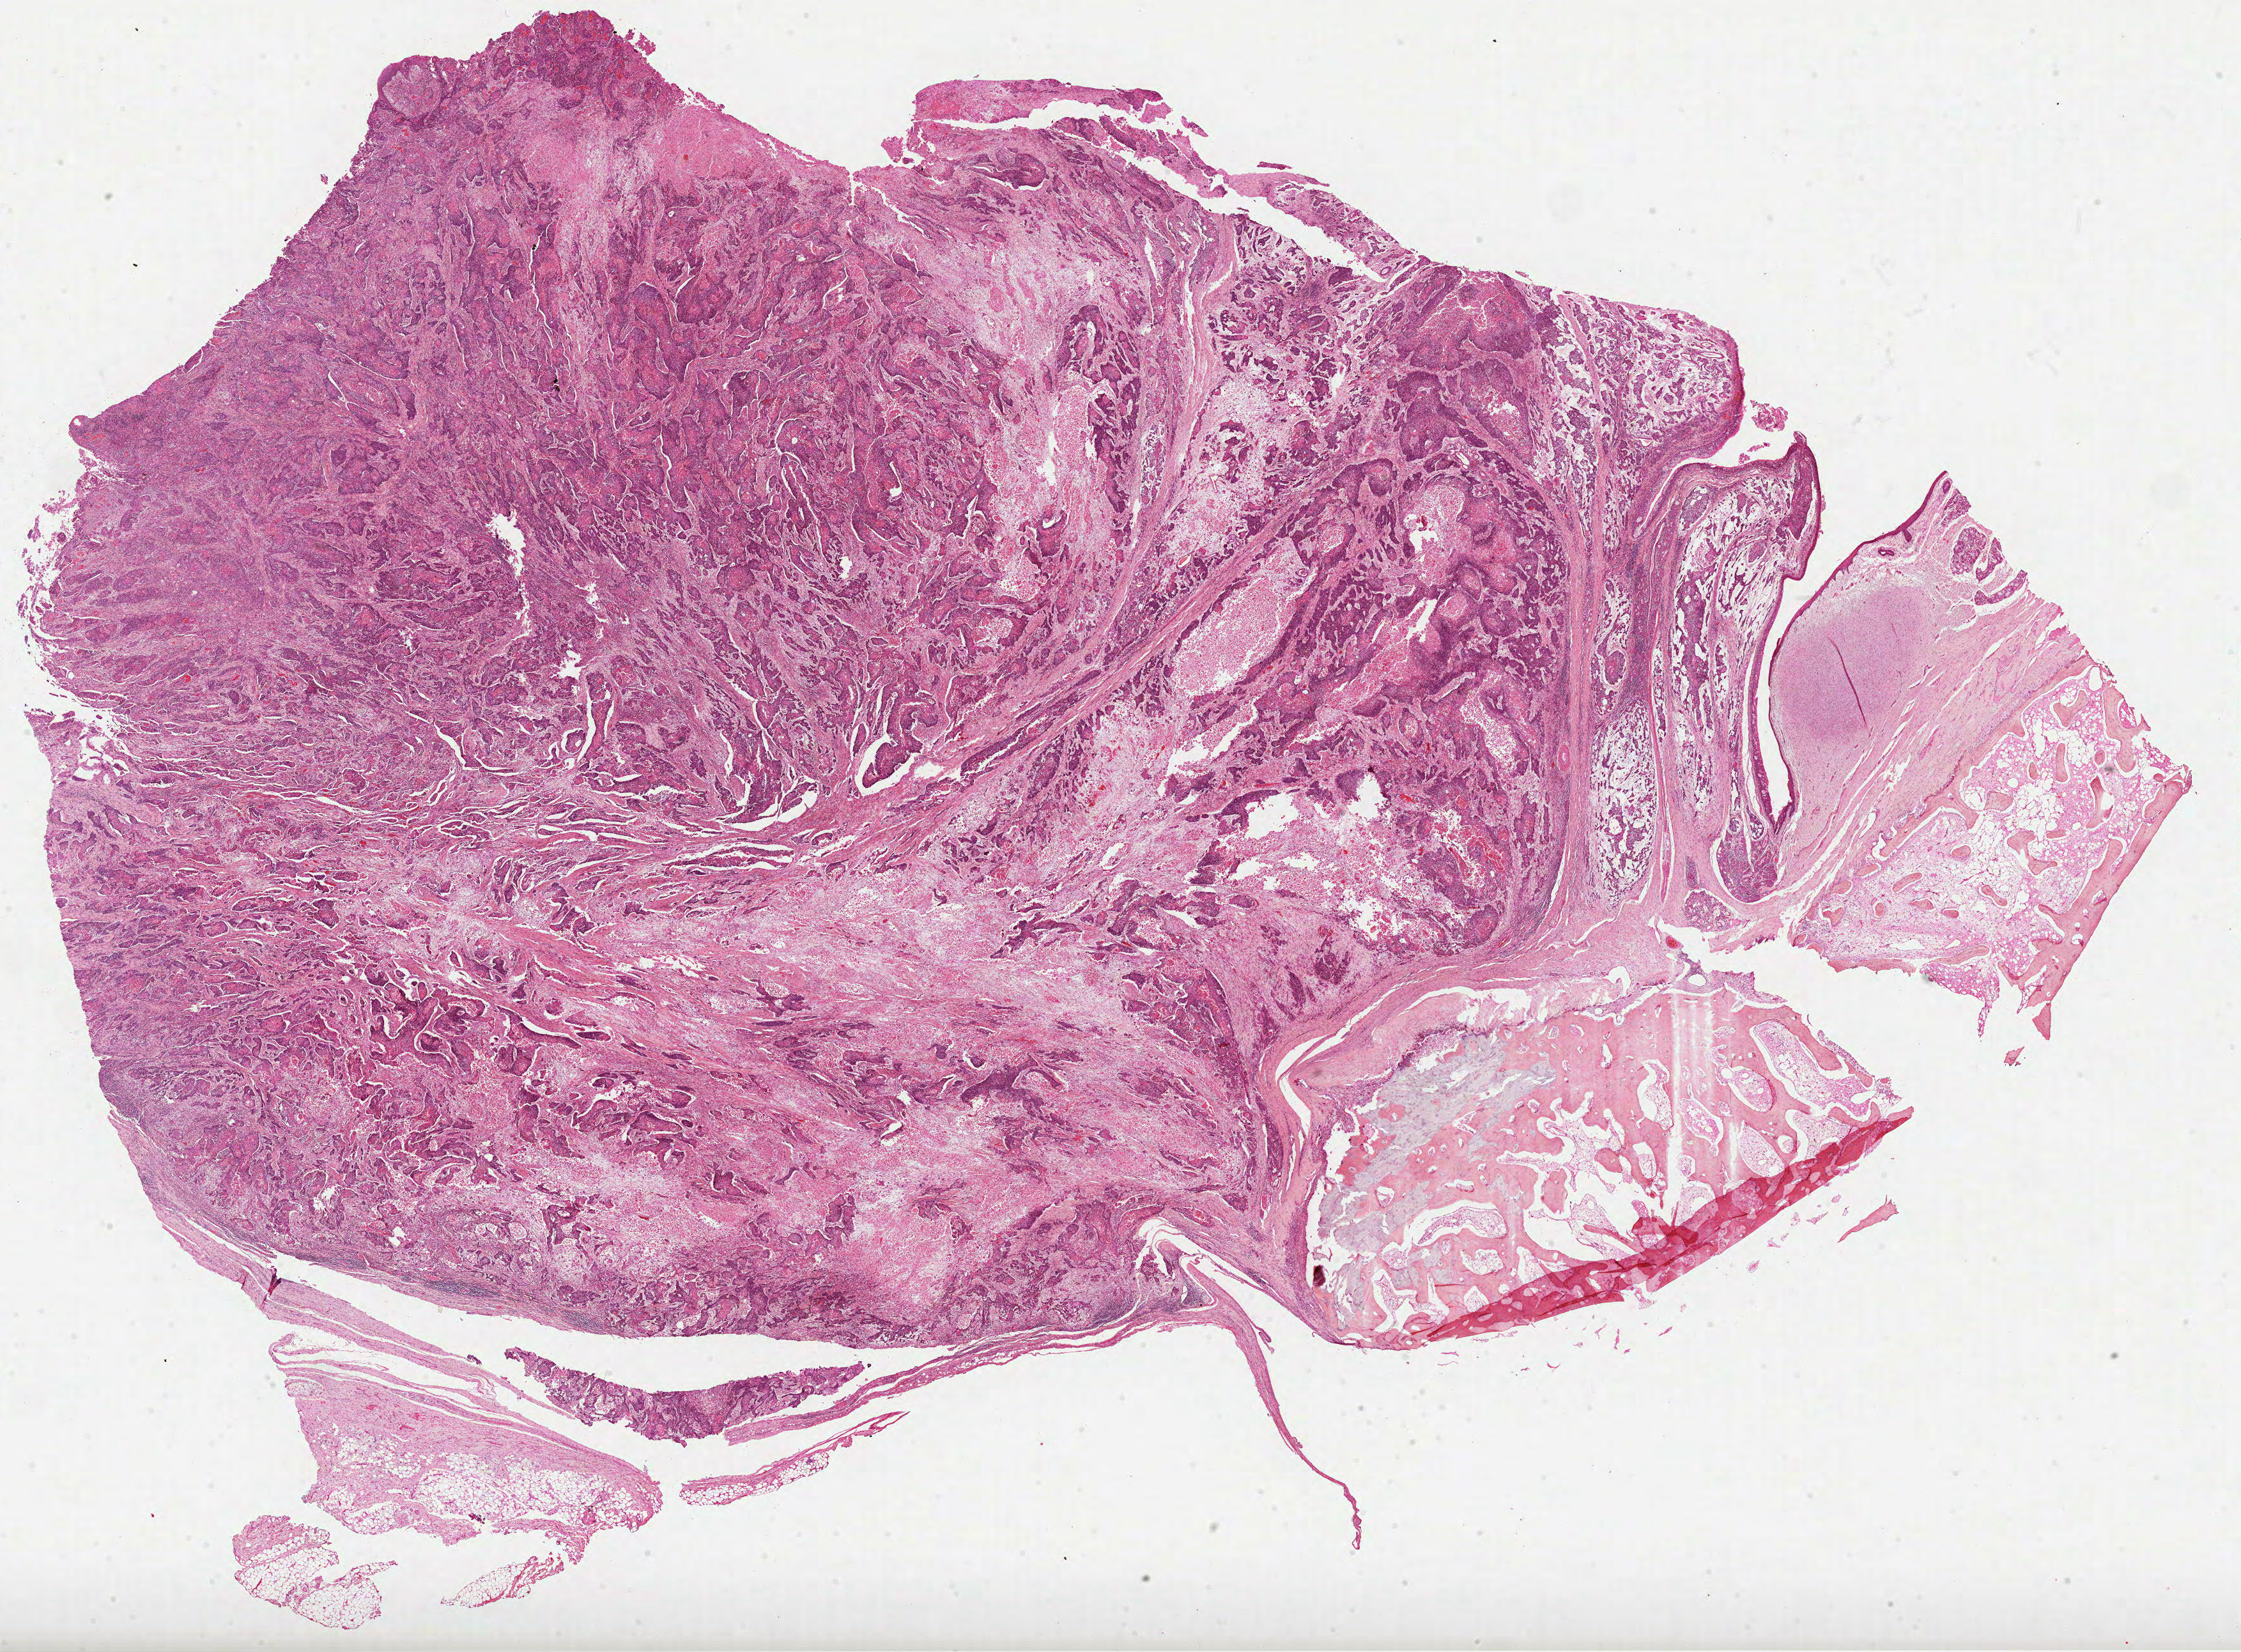
H&E-stained whole-slide image — a low-resolution overview of the entire scanned area, about 28.3 x 20.8 mm. FFPE section. Sample: primary tumour, head and neck. Patient: male, age at initial diagnosis 67 years. Histologic grade: G3 (poorly differentiated).
* pathologic diagnosis: Squamous cell carcinoma, NOS
* lymph nodes positive (case pathology): 2 of 48 examined
* TNM: T3 N2c
* AJCC pathologic stage: IVA (7th edition)